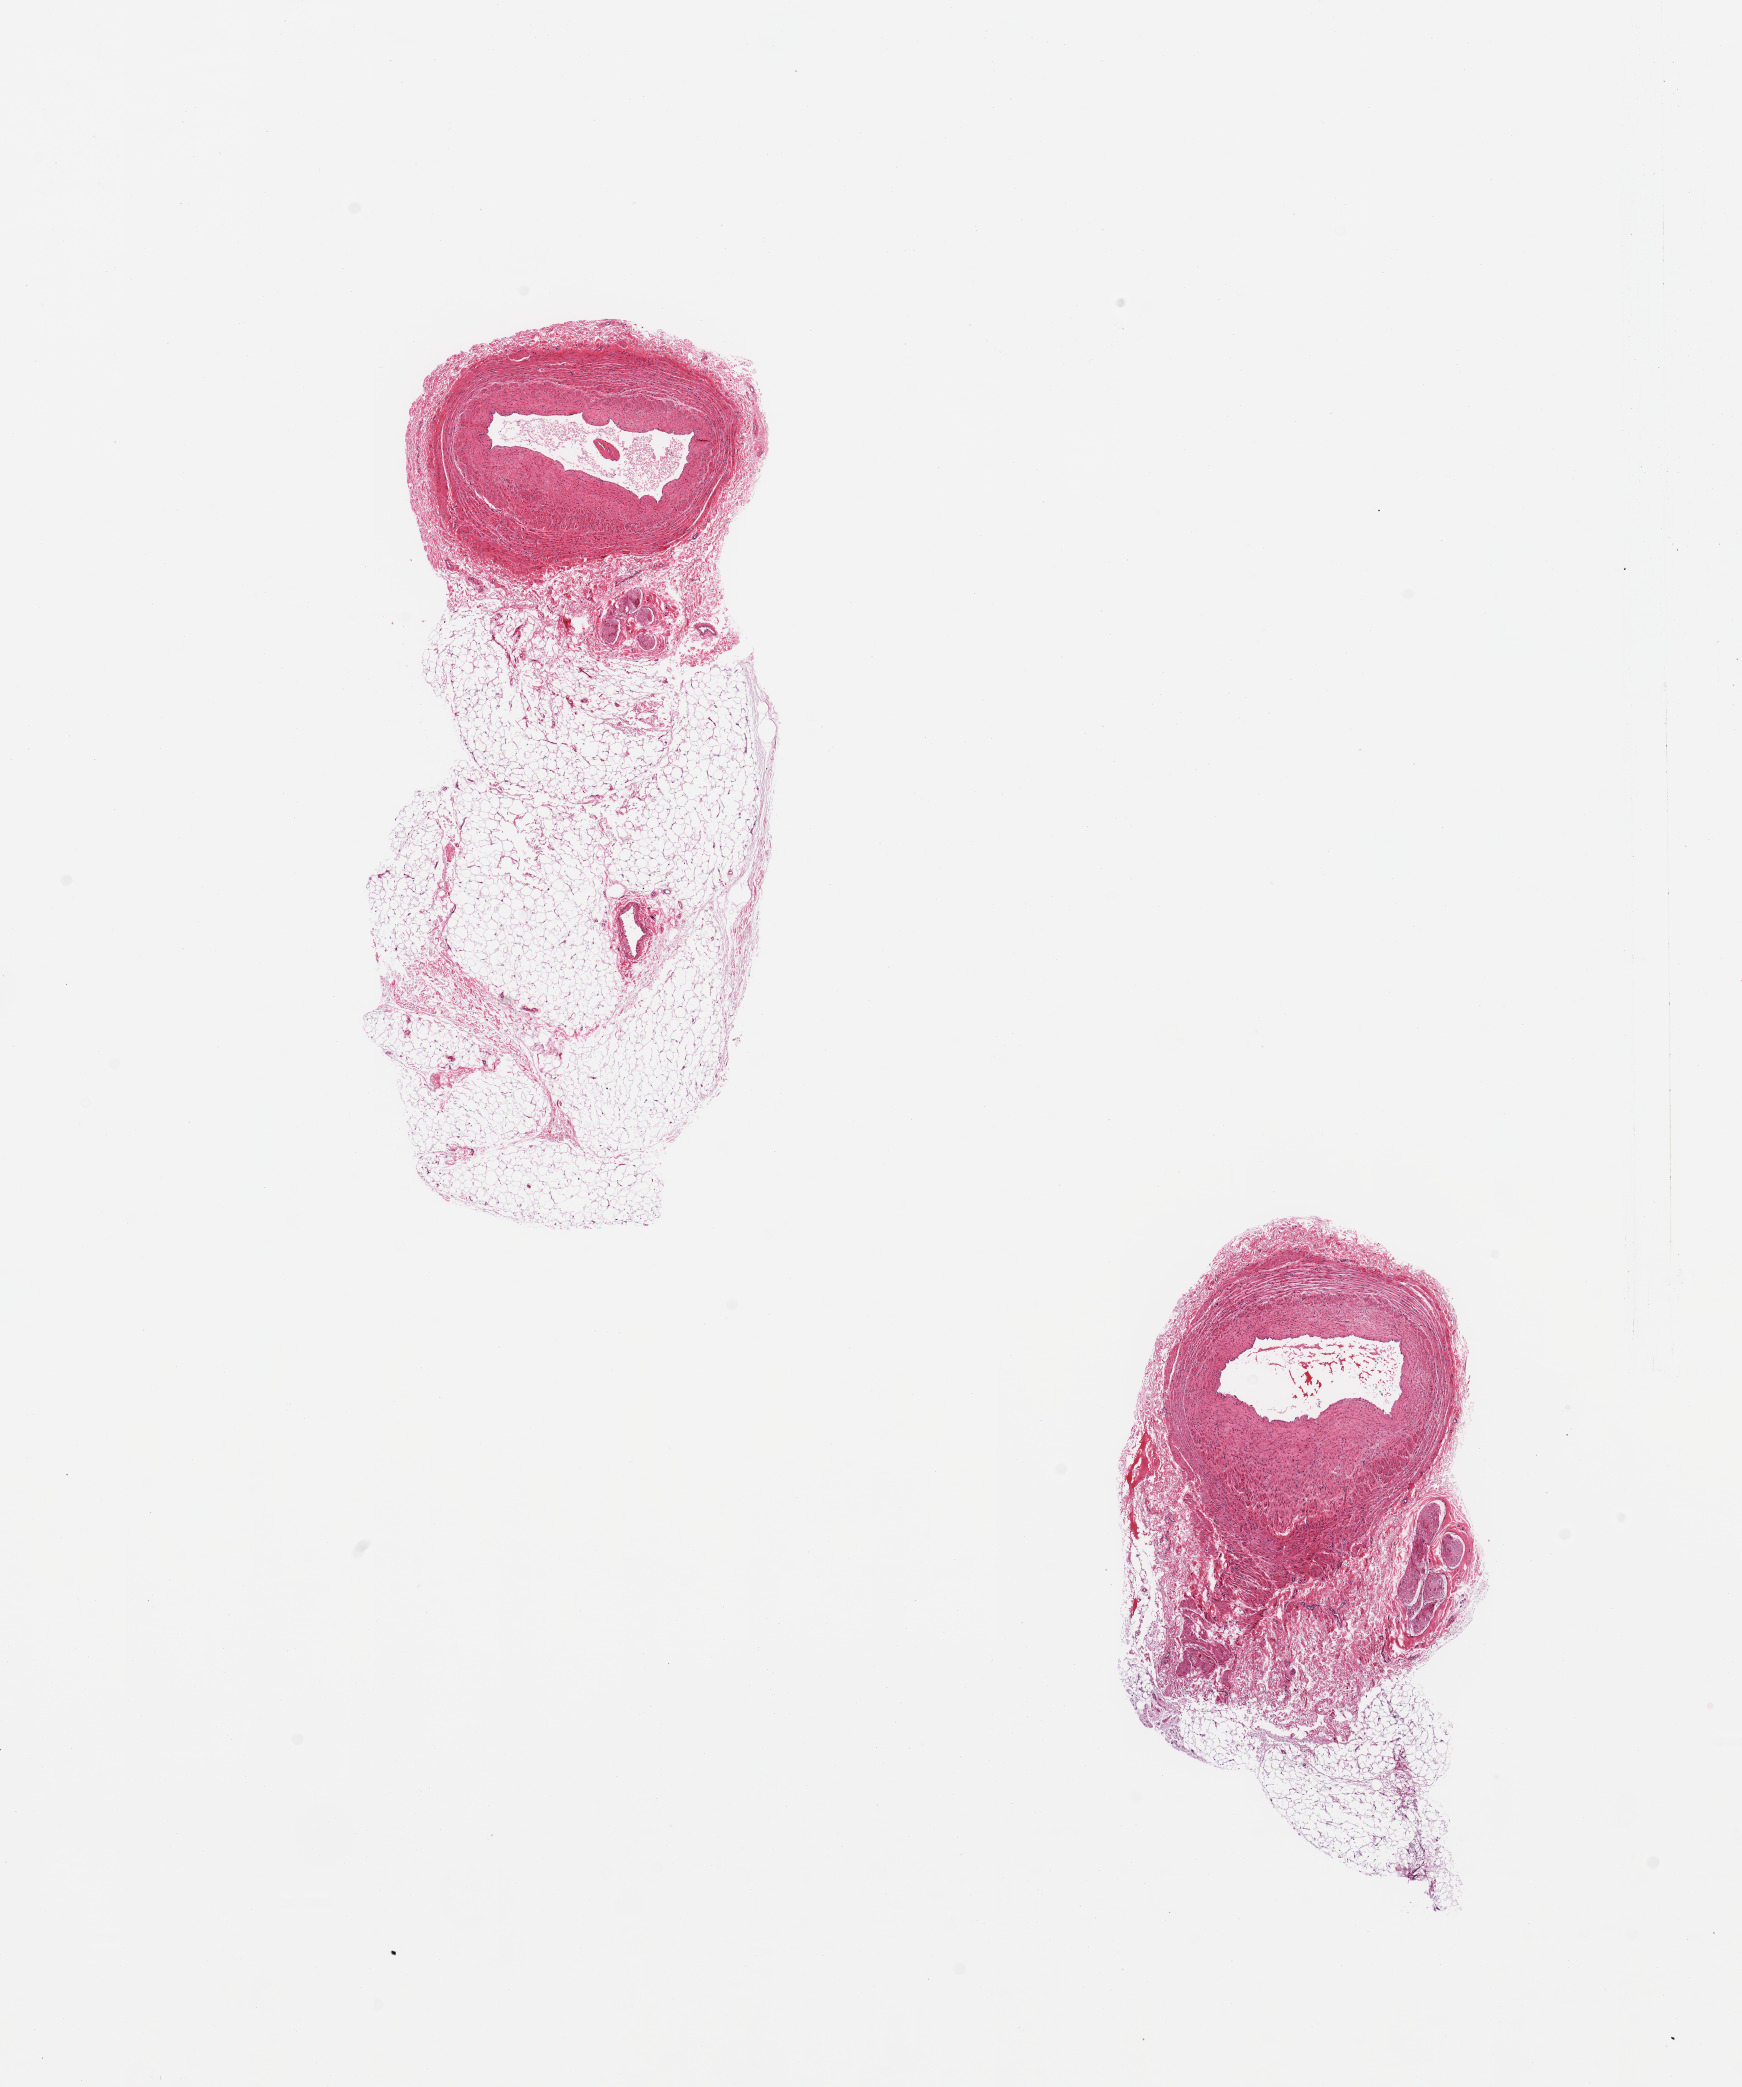
Digitized haematoxylin and eosin-stained section, shown as a low-resolution overview of the whole scanned area (about 13.8 x 16.5 mm, slide scanned at 20x), PAXgene-fixed, paraffin-embedded tissue, section of tibial artery (target tissue), tissue donor sample.
- reviewer comment on this tissue sample: 2 pieces adherent nubbins of fat up to ~5mm, minimal atherosis